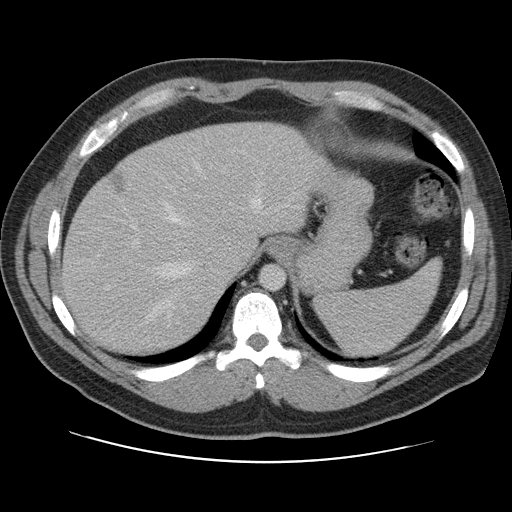
Contrast-enhanced abdominal CT, one axial slice; slice 86 of 109 in the series (ordered by position); 120 kVp; intravenous contrast given; soft-tissue window (W 400 / L 40 HU); 512 × 512 image matrix. Male patient, age 35 years. From the clinical record (not read from this slice): diagnosis: colorectal cancer liver metastases, imaged before liver resection; multiple liver metastases: yes.
Structures marked on this image (expert manual segmentation):
- hepatic veins: box from (x=139, y=159) to (x=271, y=327) px
- liver: (x=63, y=123)–(x=315, y=355)
- planned liver remnant (the part of the liver to remain after resection): (x=63, y=123)–(x=315, y=355)
- portal vein (with intrahepatic branches): (x=126, y=163)–(x=213, y=272)
- liver metastasis: (x=110, y=173)–(x=125, y=193)